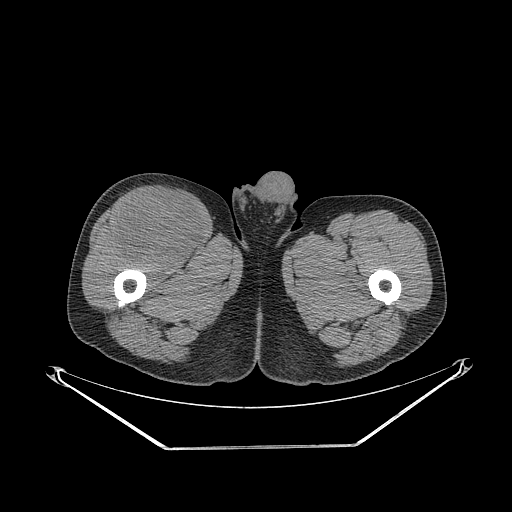
CT of an extremity soft-tissue mass (from a PET/CT study), one axial slice; position 290 of 311 along the scan axis; soft-tissue window (W 400 / L 40 HU); 3.75 mm slice thickness; 512 × 512 image matrix, field of view 500 × 500 mm. Male patient. From the clinical record (not read from this slice): histological type: pleiomorphic leiomyosarcoma; grade: intermediate; site of the primary tumour: right thigh.
Annotated regions visible in this slice (expert contour drawn on MRI and transferred to this co-registered scan by the dataset authors):
- gross tumour volume including surrounding oedema: box from (x=114, y=190) to (x=206, y=266) px
- gross tumour volume (mass): (x=116, y=190)–(x=206, y=266)